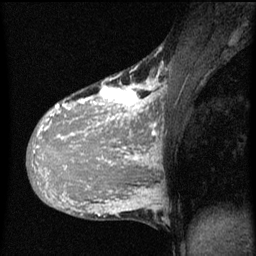
Breast MRI (dynamic contrast-enhanced), one sagittal slice. Slice 29 of 60 in the series (ordered by position). Dynamic contrast-enhanced series, image 2 of 3 at this slice position (ordered by acquisition). 1.5 T. TE 4.2 ms, TR 8 ms. 2 mm slice thickness. 256 × 256 image matrix. Patient: female, 36 years.
Outlined on this slice (semi-automatic segmentation, software-assisted and operator-edited):
- analysis volume of interest (the breast-tissue region the enhancement analysis was run in; not a lesion): box from (x=32, y=68) to (x=167, y=161) px
- tumour enhancement mask (voxels above the 70 % enhancement threshold inside the analysis volume of interest): (x=32, y=70)–(x=165, y=161)